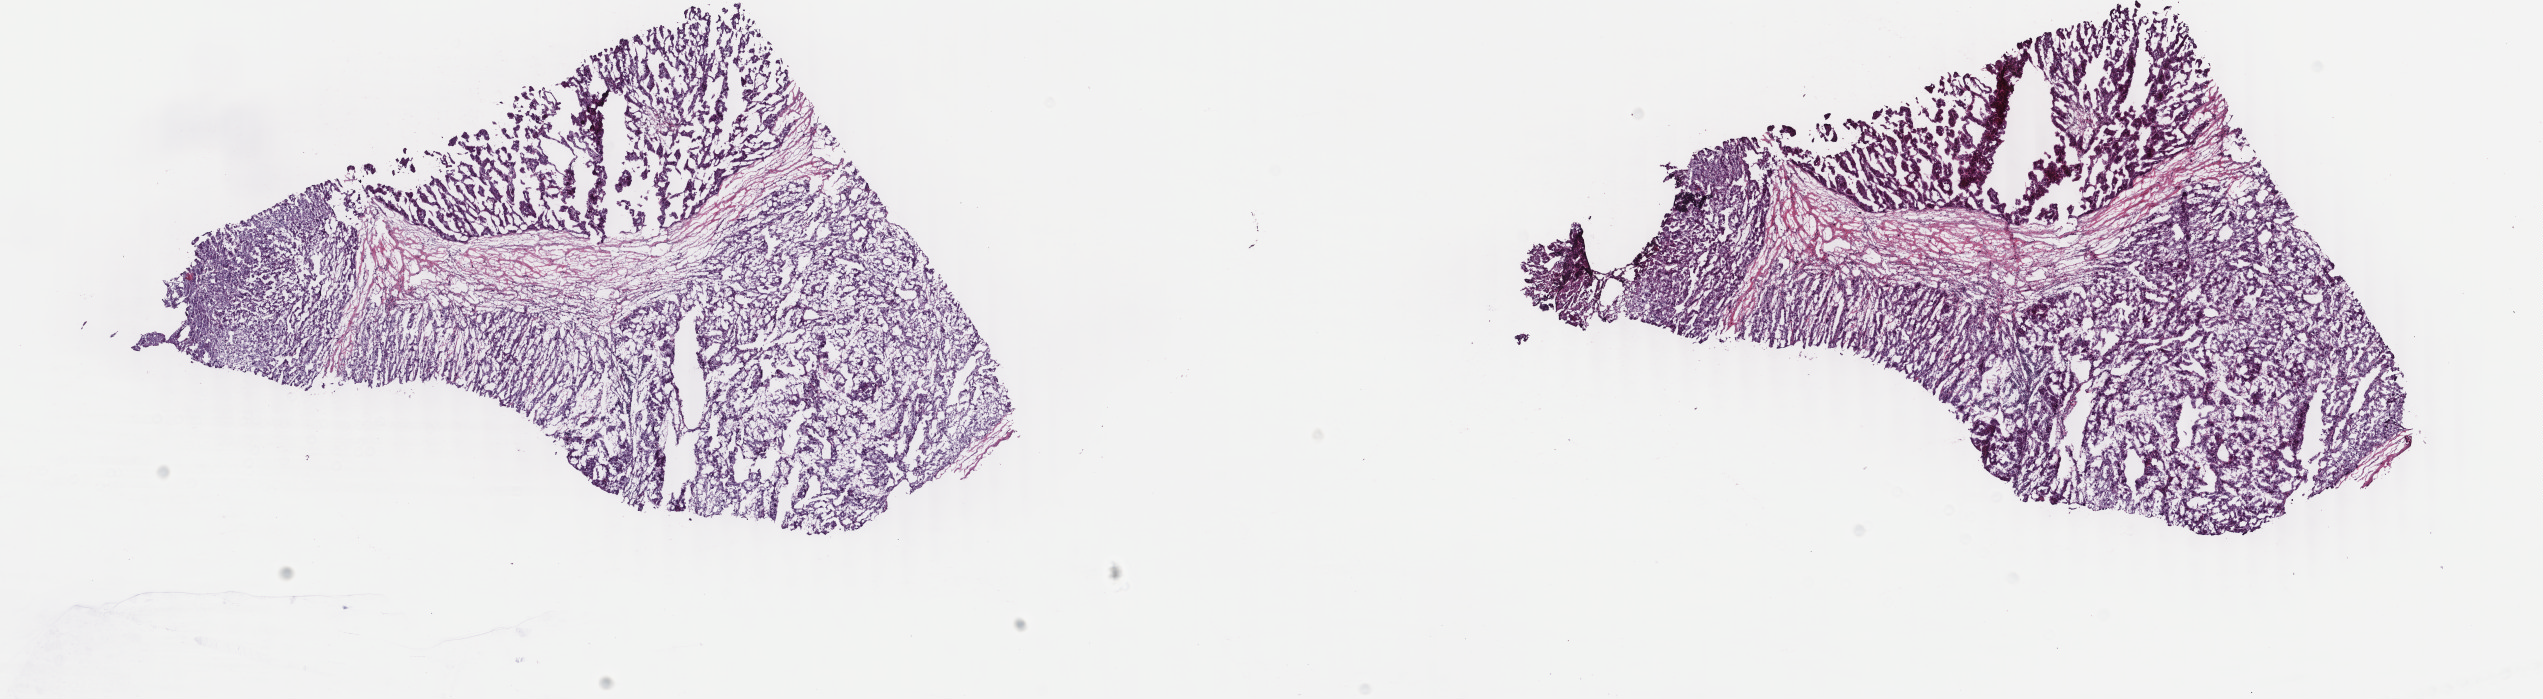
Whole-slide histology image, H&E-stained, a low-resolution overview of the entire scanned area, about 20.2 x 5.6 mm, frozen section from the top of the tissue portion, sample: primary tumour, liver. Male patient; age at initial diagnosis 68 years. Composition of this section per pathologist review: tumour cells 85%, tumour nuclei 85%.
Histologic diagnosis: Hepatocellular carcinoma, NOS.